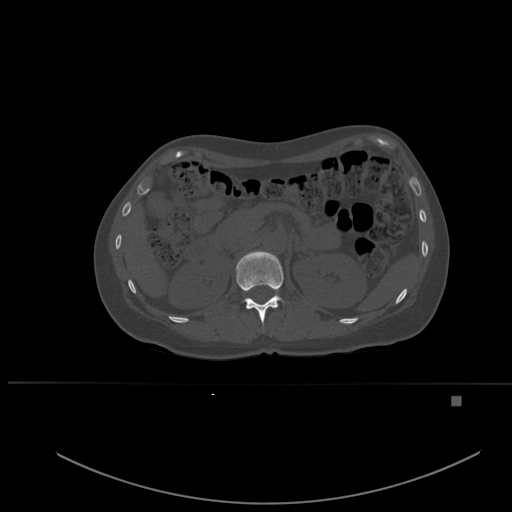
CT including the spine, one axial slice. Bone window (W 1800 / L 400 HU). 512 × 512 image matrix, field of view 443 × 443 mm. Female patient, age 49 years. From the clinical record (not read from this slice): primary cancer: breast.
Annotated regions visible in this slice (semi-automatic segmentation, software-assisted and operator-edited):
- T12 vertebra: bounding box <236,251,284,326> (left, top, right, bottom; pixels)